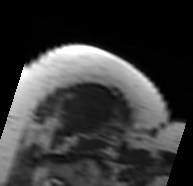
MRI of an extremity soft-tissue mass, one axial slice. Slice 62 of 91 in the series (ordered by position). MR volume resampled by the dataset authors to the PET/CT grid (not the native acquisition matrix). 193 × 186 image matrix. Female patient. Case-level facts recorded for this patient, not image findings: histological type: malignant solitary fibrous tumor; grade: intermediate; site of the primary tumour: right thigh.
Outlined on this slice (expert contour drawn on MRI and transferred to this co-registered scan by the dataset authors):
- gross tumour volume including surrounding oedema: bounding box (x1, y1, x2, y2) in pixels: (45, 92, 119, 150)
- gross tumour volume (mass): (63, 97, 112, 134)